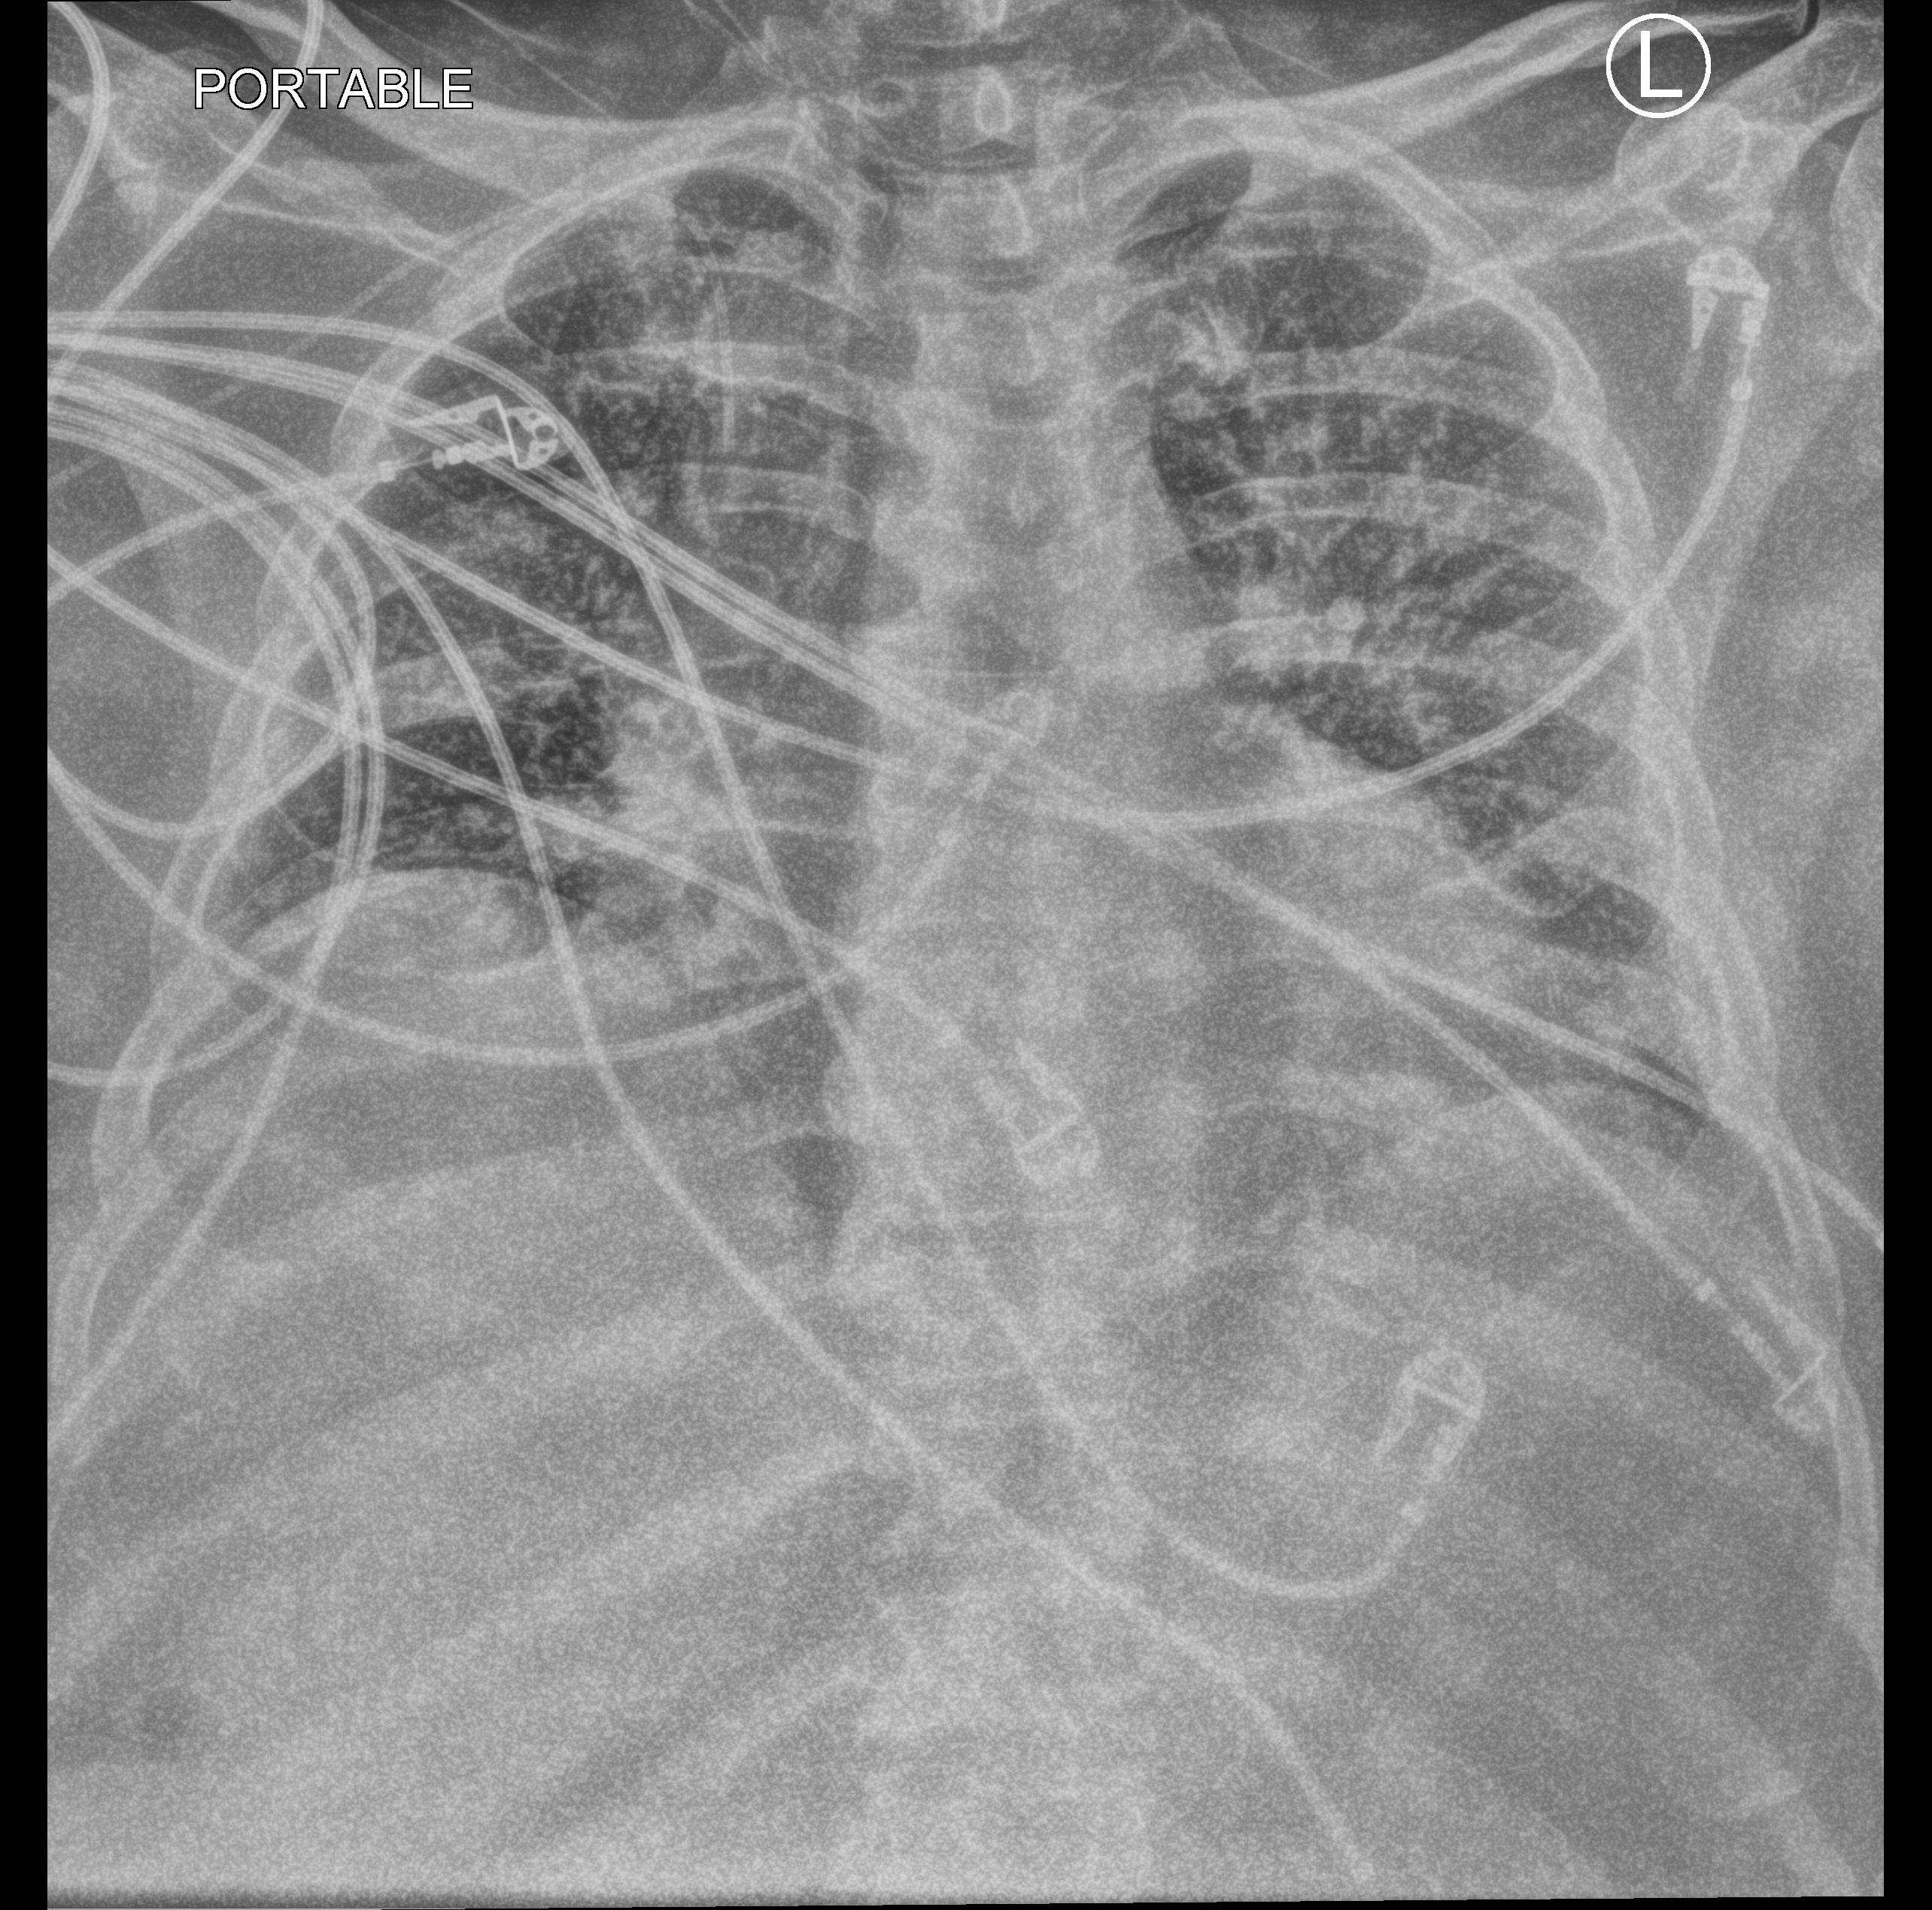
Portable chest radiograph, anteroposterior (AP) projection. Patient hospitalised with COVID-19; male, aged 18–59 years.
Admission-level facts for this patient (not findings on this image; timing relative to this image not recorded):
- chronic kidney disease (admission record): no
- mechanically ventilated during this hospital stay: yes
- other chronic lung disease (admission record): no